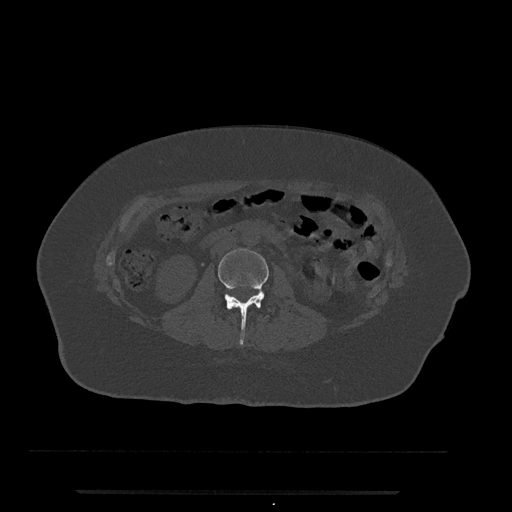
CT including the spine, one axial slice; bone window (W 1800 / L 400 HU); 512 × 512 image matrix, field of view 440 × 440 mm. Patient: female, 51 years. From the clinical record (not read from this slice): primary cancer: neuro; vertebrae with lytic lesions (as recorded): T8.
Annotated regions visible in this slice (semi-automatic segmentation, software-assisted and operator-edited):
- L2 vertebra: bounding box [x1, y1, x2, y2] px = [218, 249, 269, 344]